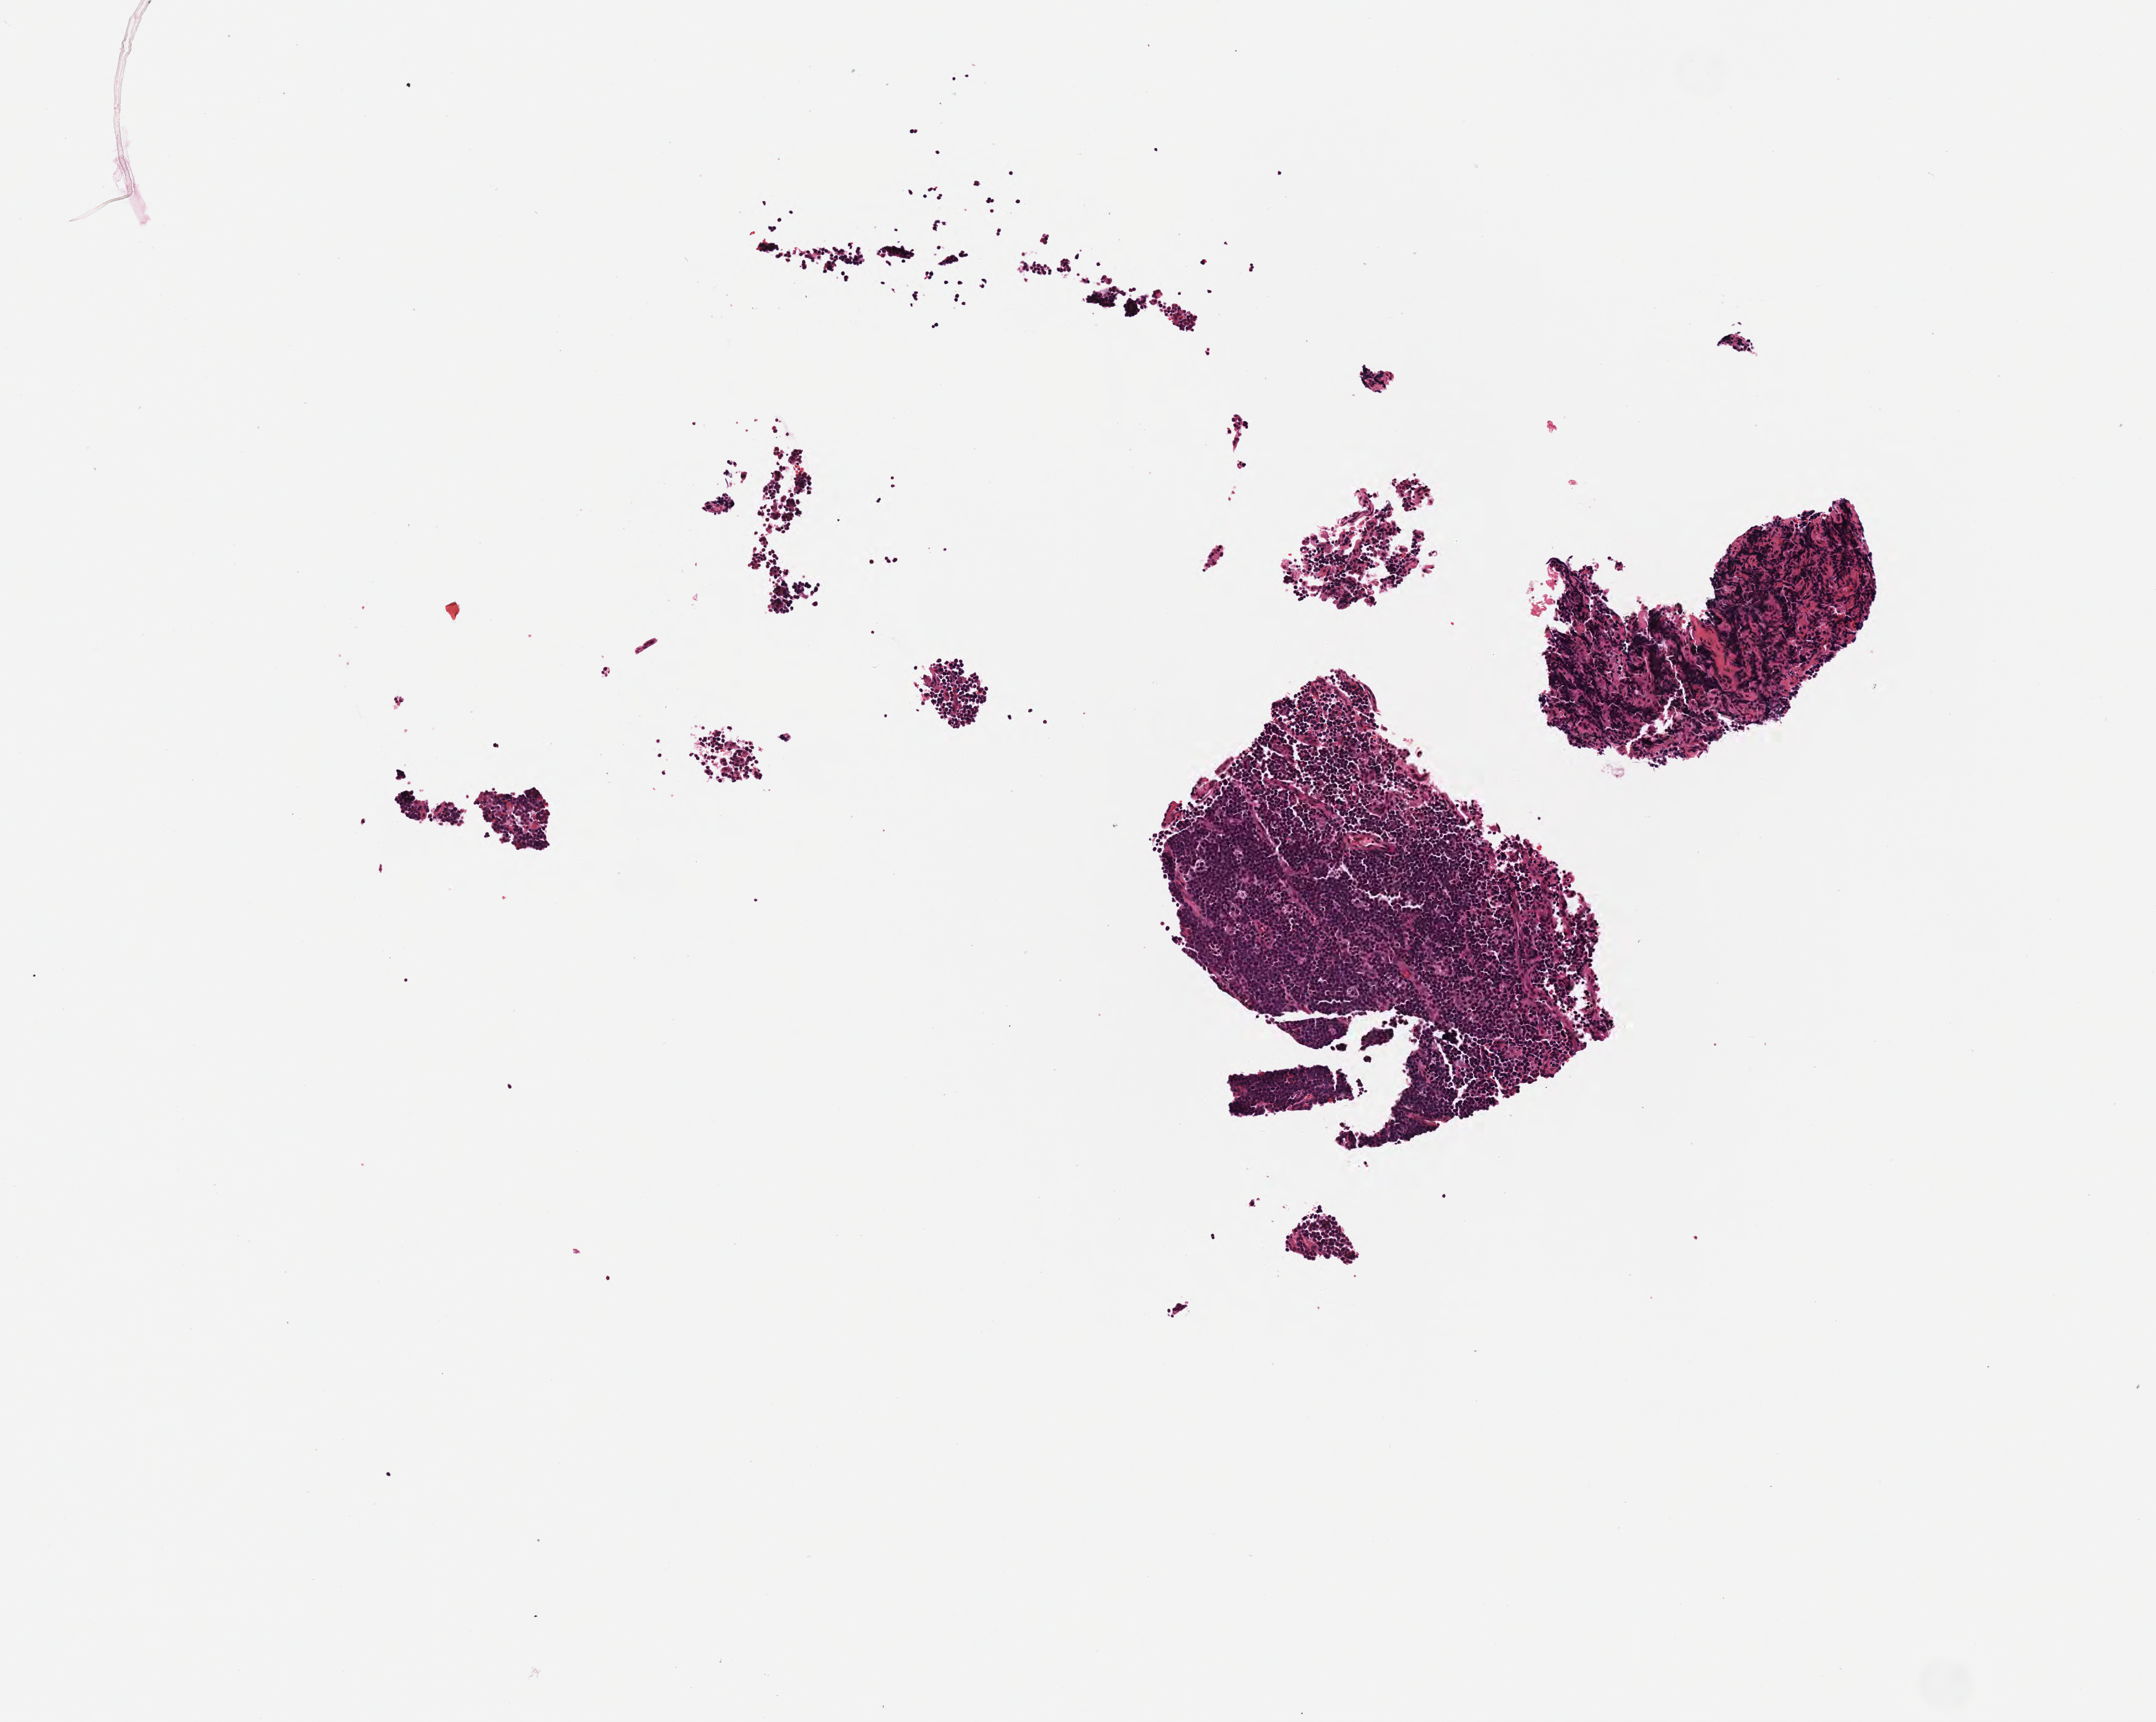
Hematoxylin and eosin (H&E) whole-slide image — shown as a low-resolution overview of the whole scanned area (about 3.5 x 2.8 mm); FFPE section; specimen: primary tumor; site: cranium. Male patient; age at initial diagnosis 6 years. Slide review estimates, as recorded: tumor cells 95%, tumor nuclei 95%, stromal cells 3%, necrosis 2%, normal cells 0%. Infiltration values recorded for this section: lymphocyte infiltration 40%, monocyte infiltration 40%, neutrophil infiltration 5%.
• diagnosis: Burkitt lymphoma, NOS
• section: bottom of the tissue portion
• Ann Arbor stage (patient): Stage IV